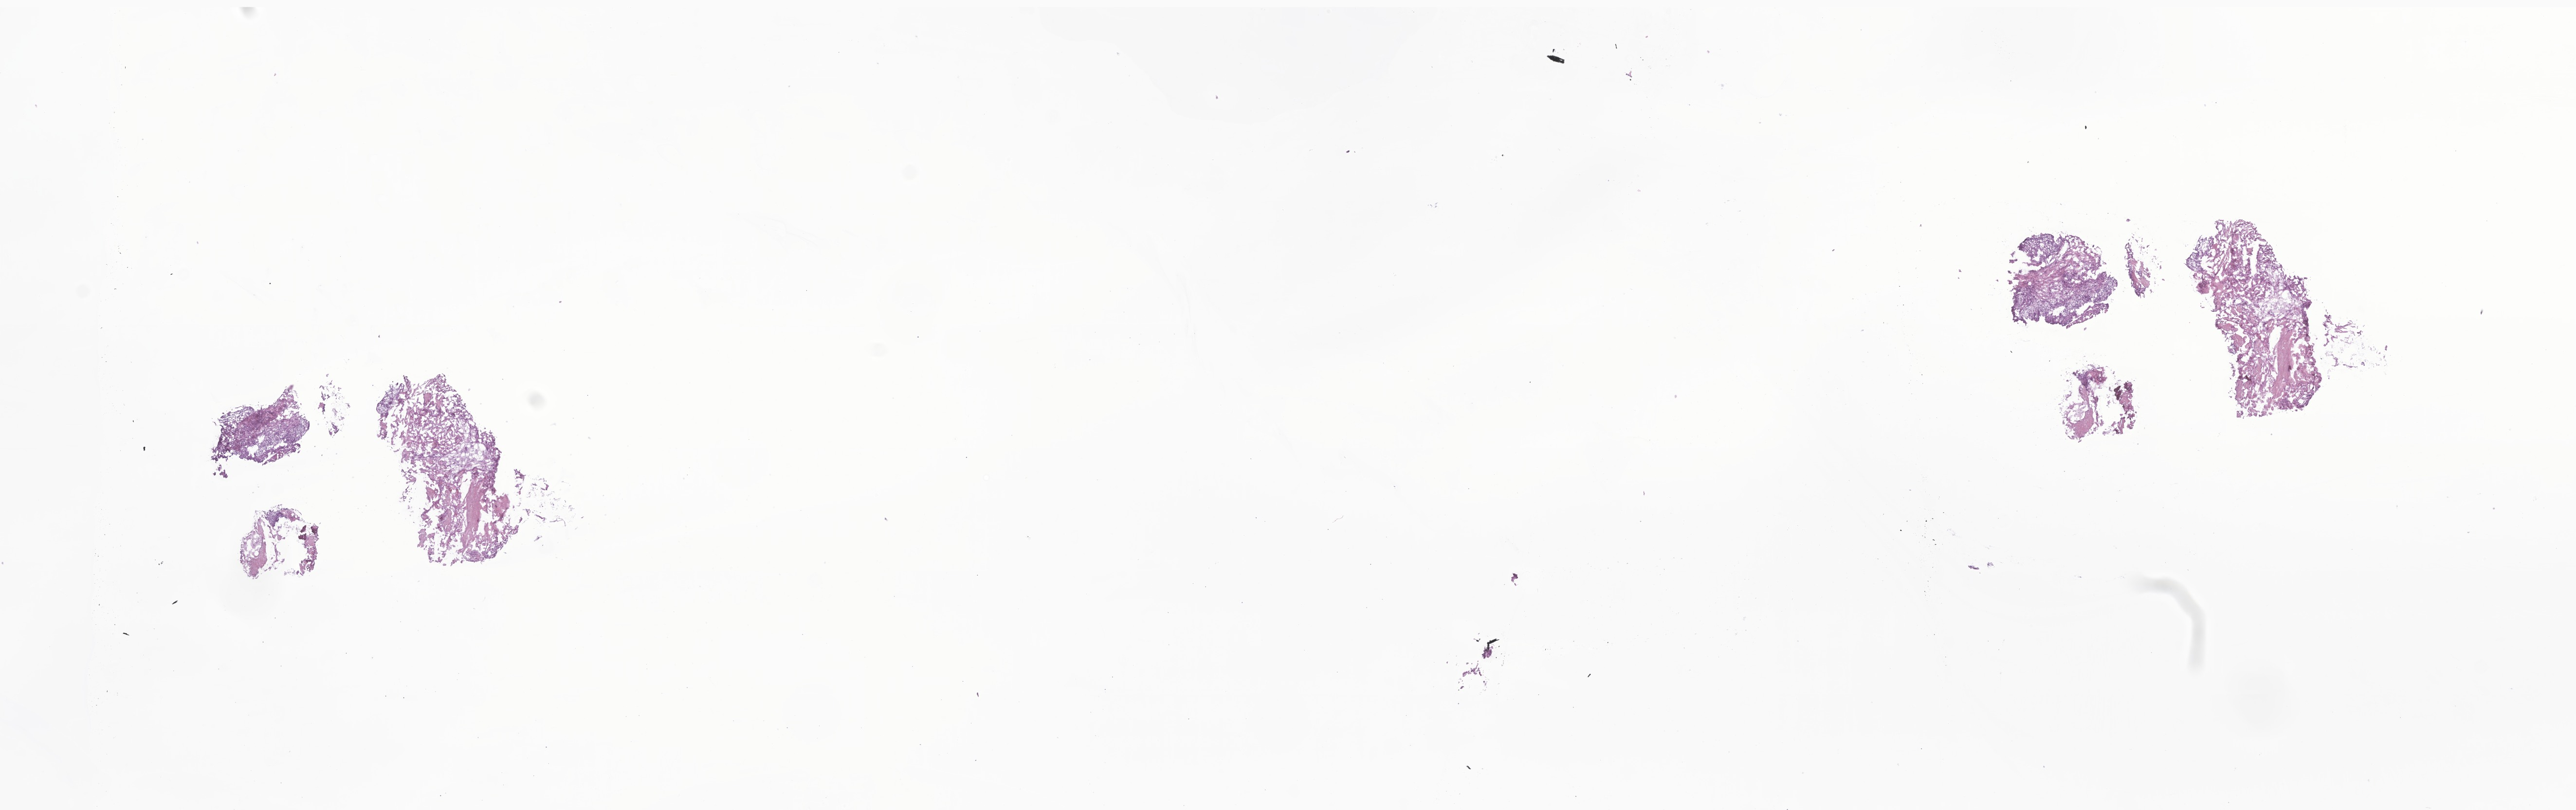
Haematoxylin and eosin whole-slide image of tumor tissue from the brain, a low-resolution overview of the entire scanned area, about 22.3 x 7.0 mm, cryosection (OCT / tissue freezing medium). Female patient, age 579 days (about 1.6 years).
Recorded diagnosis: Craniopharyngioma, NOS.